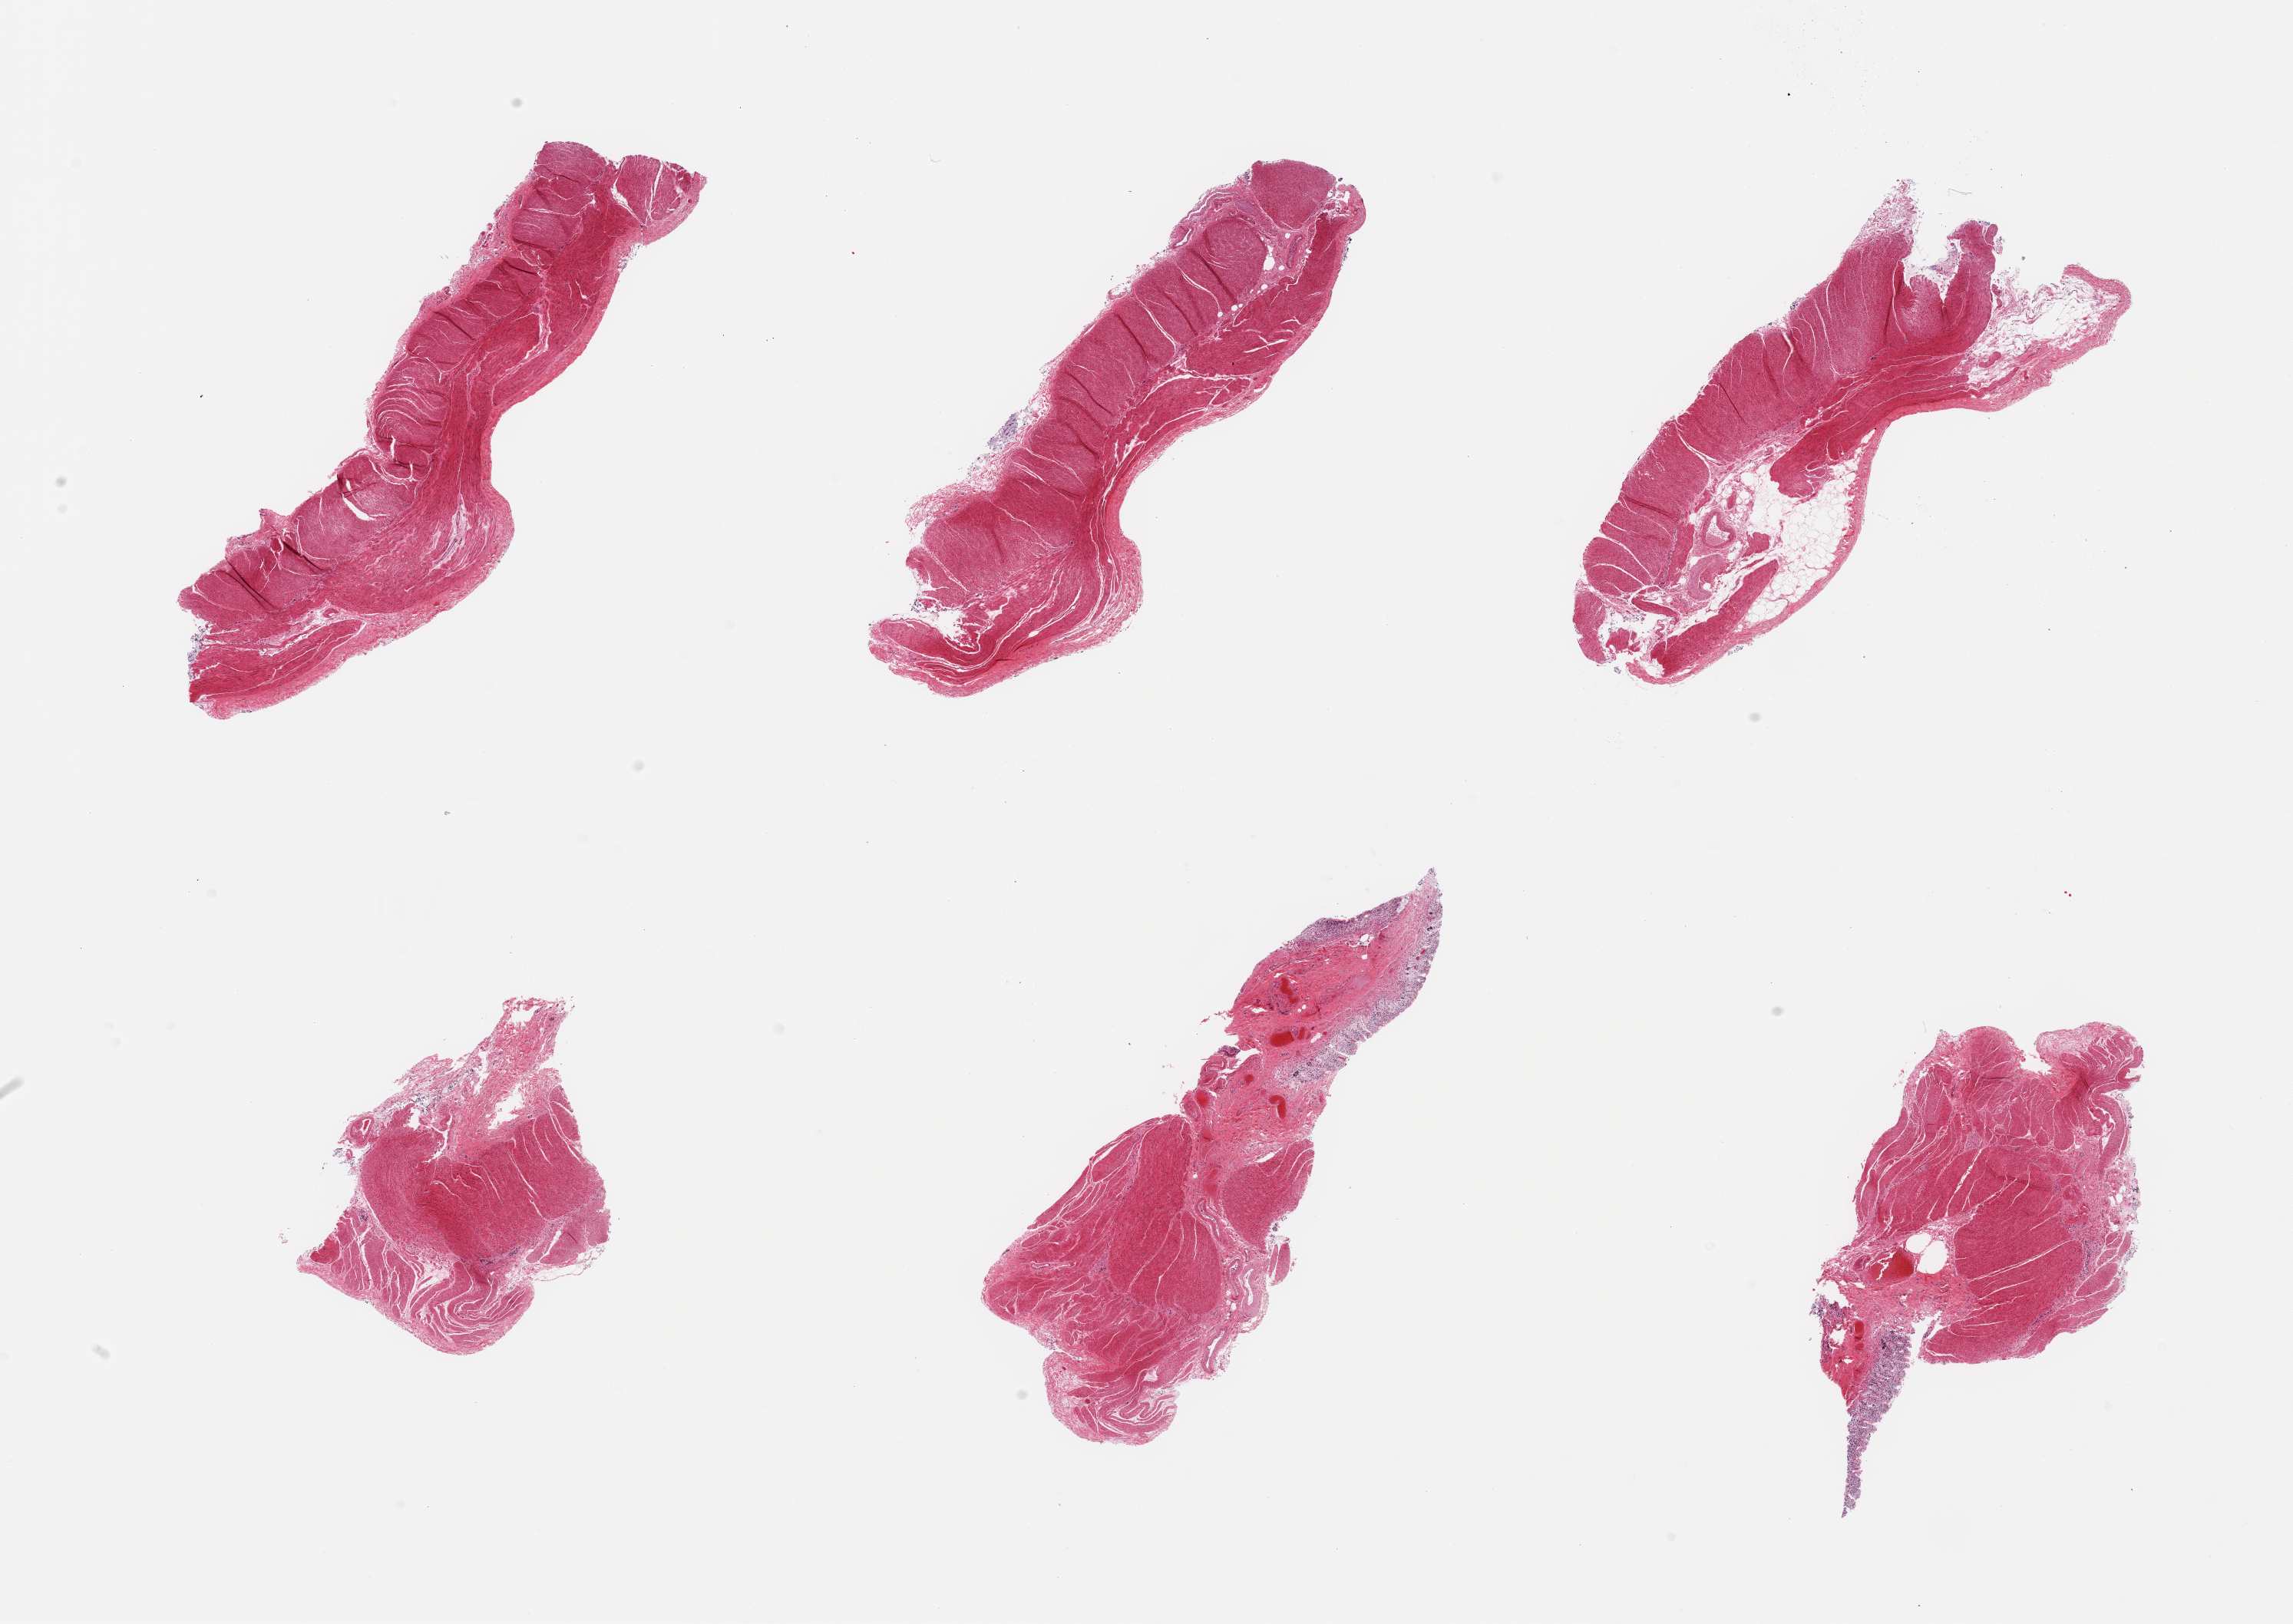
Haematoxylin and eosin whole-slide image, whole scanned area (about 23.6 x 16.7 mm, acquisition: 20x scan) shown as a low-resolution overview; PAXgene-fixed paraffin-embedded (PFPE) section; sampled site (target tissue): sigmoid colon; donor tissue sample. Donor sex: male.
Reviewer comment on this tissue sample: 6 pieces; 2 pieces contain submucosa and mucosal remnants.